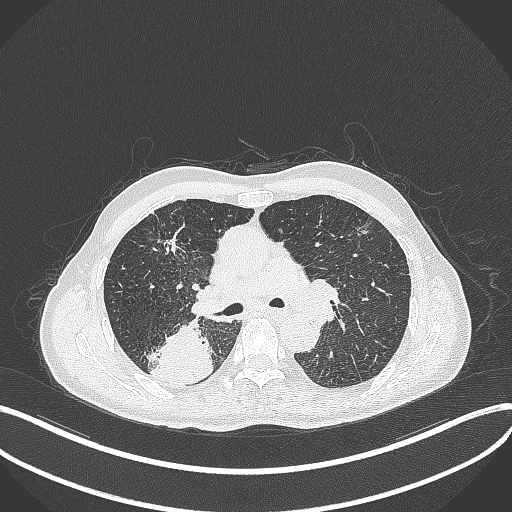
Chest CT, one axial slice. Slice 282 of 428 in the series (ordered by position). Lung window (W 1500 / L -600 HU). 512 × 512 image matrix, field of view 400 × 400 mm. Male patient, age 79 years. From the clinical record (not read from this slice): clinical TNM (as recorded): T3 N0 M0.
Structures marked on this image (bounding box drawn by a radiologist):
- lung tumour (recorded histology: adenocarcinoma): bounding box <140,324,212,385> (left, top, right, bottom; pixels)